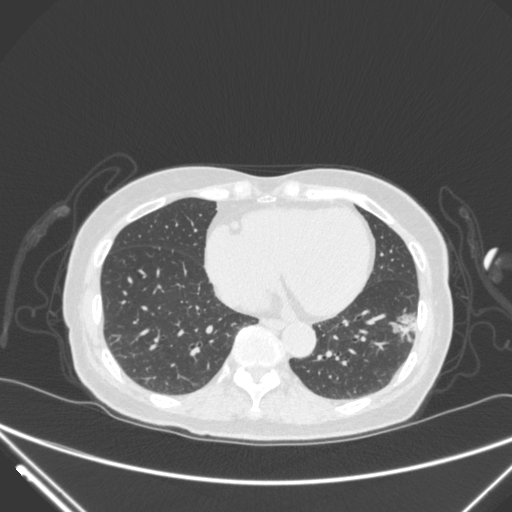
Chest CT, one axial slice; slice 106 of 310 in the series (ordered by position); 120 kVp; lung window (W 1500 / L -600 HU); 1 mm slice thickness; 512 × 512 image matrix, field of view 377 × 377 mm. Female patient, age 82 years. Case-level facts recorded for this patient, not image findings: clinical TNM (as recorded): T1c N0 M0; histopathological grade: G2.
Outlined on this slice (bounding box drawn by a radiologist):
- lung tumour (recorded histology: adenocarcinoma): bounding box [x1, y1, x2, y2] px = [384, 293, 419, 343]